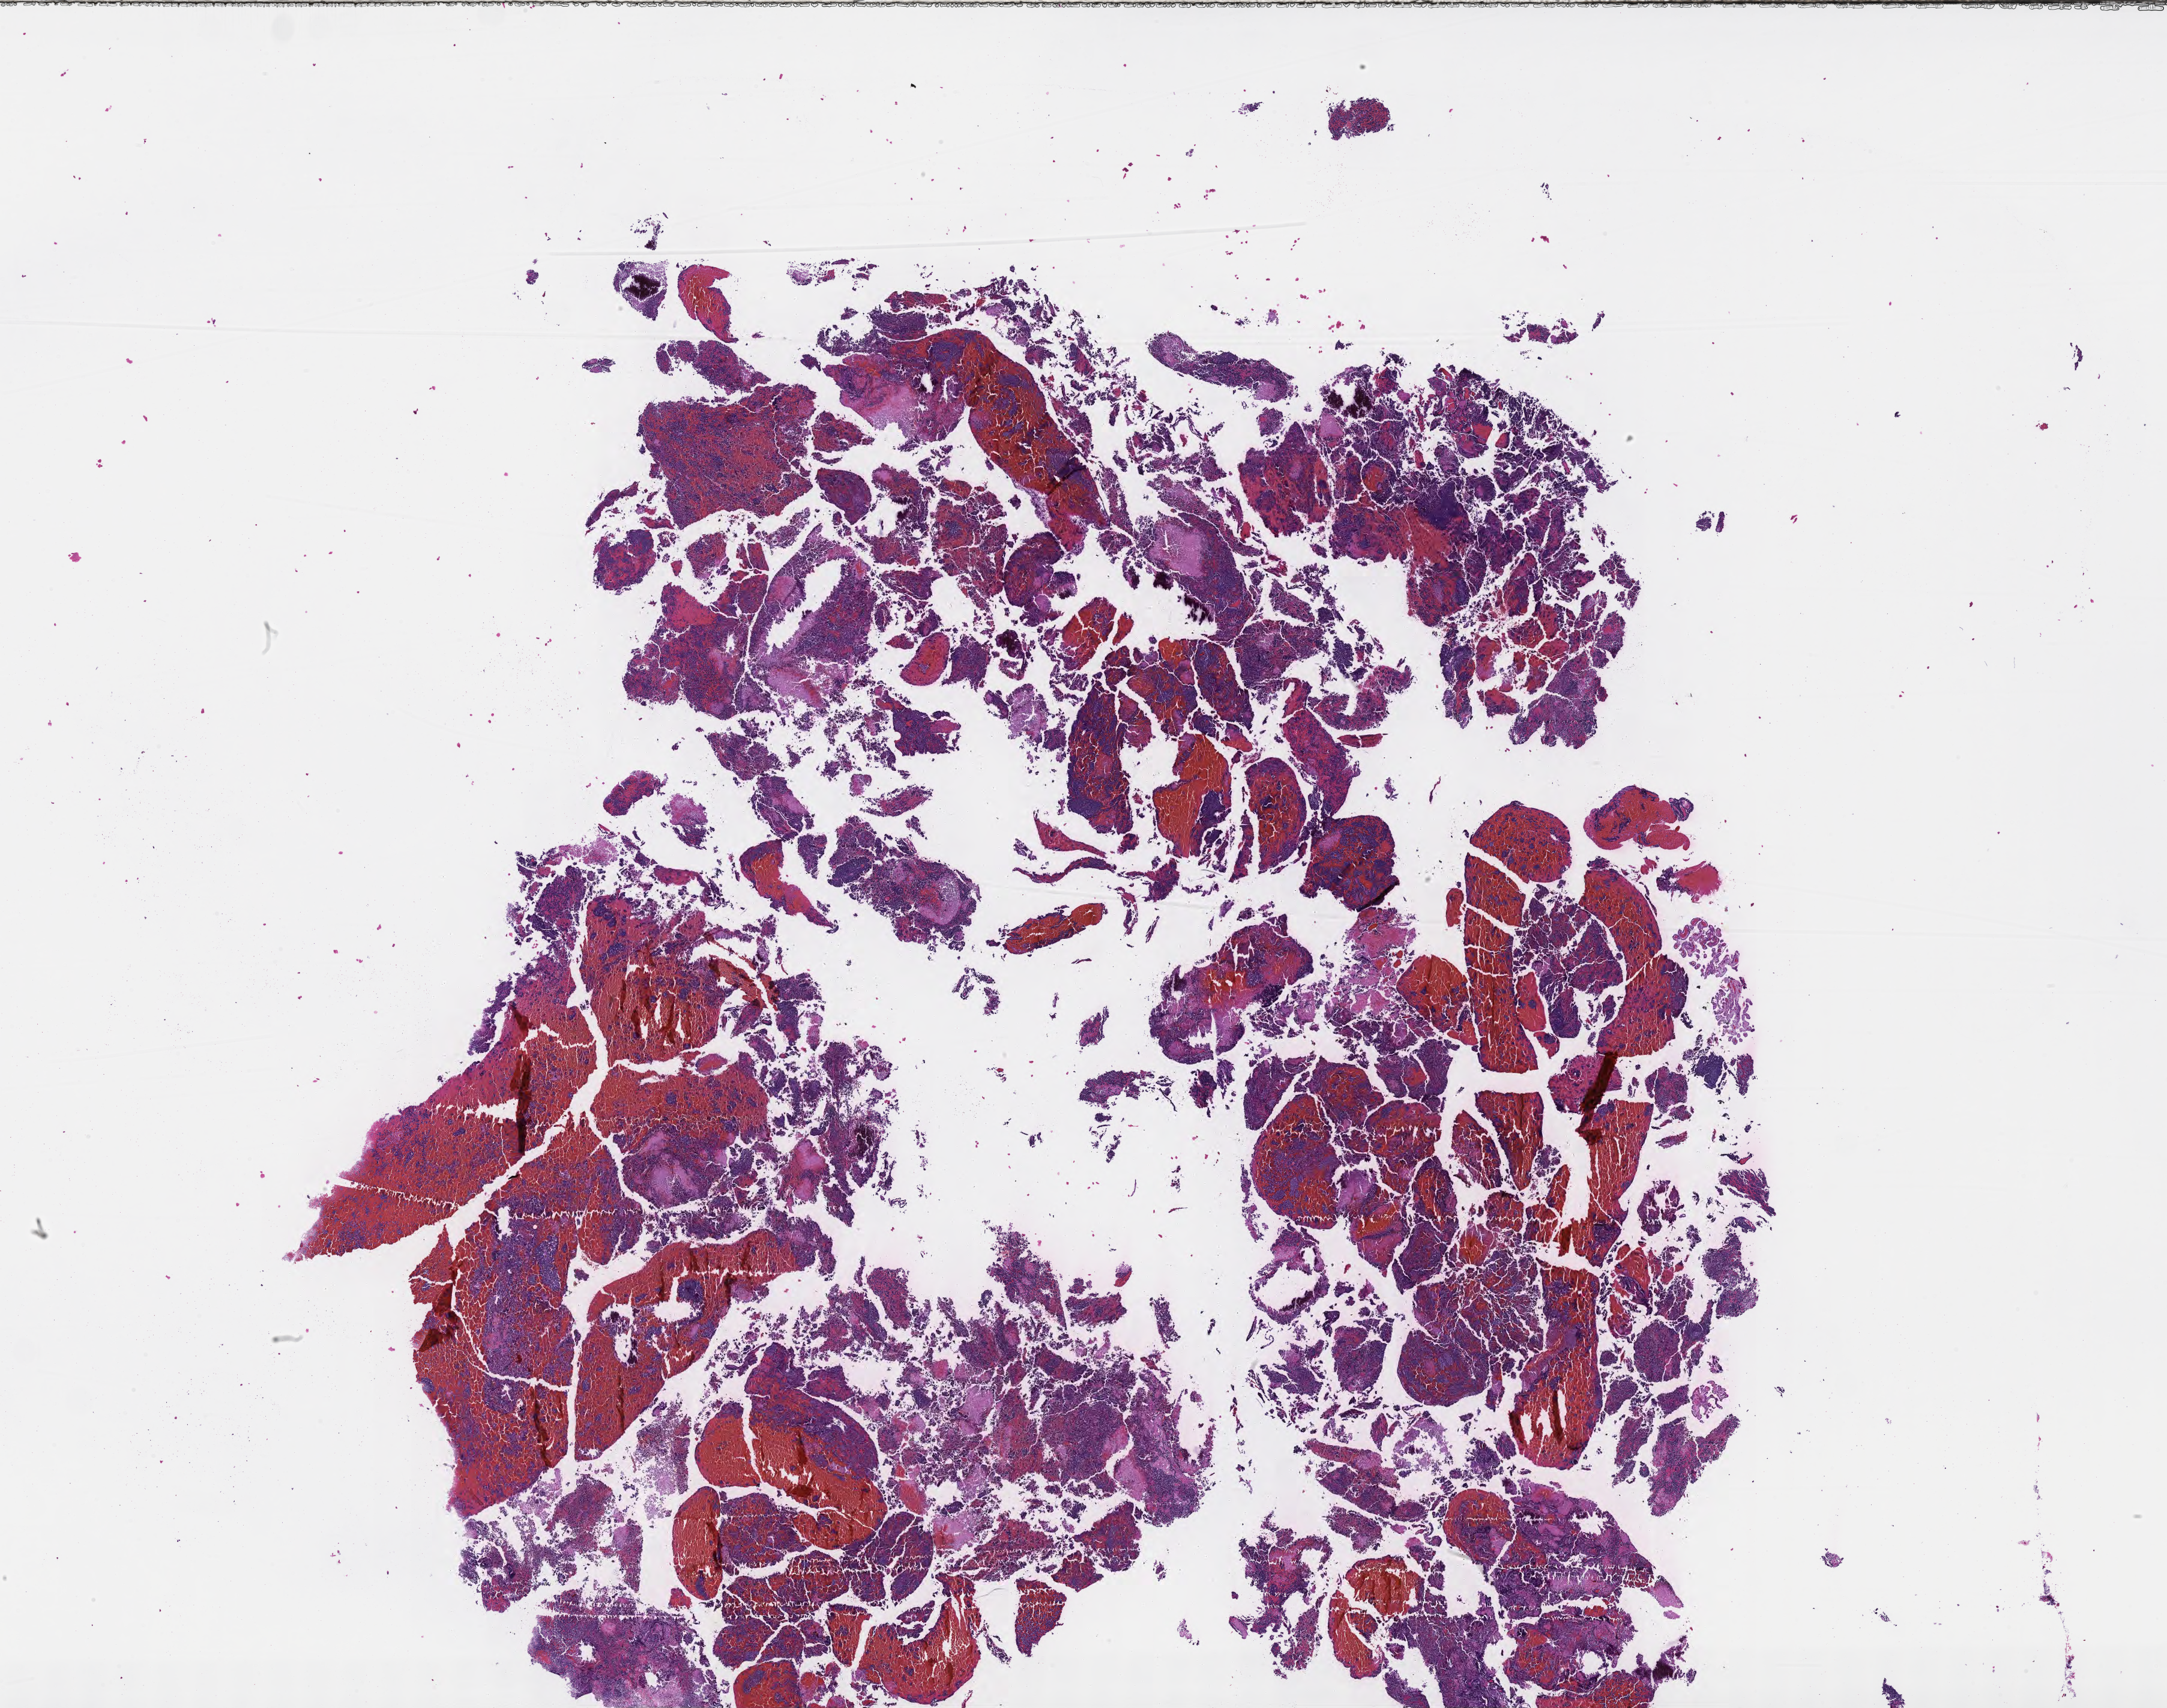
Whole-slide image, hematoxylin and eosin (H&E) stain of tumor tissue from the pineal gland — a low-resolution overview of the entire scanned area, about 29.2 x 23.0 mm, FFPE section. Patient: female, age 146 months (12 years 2 months).
Diagnosis (ICD-O-3 morphology term): Pineoblastoma.